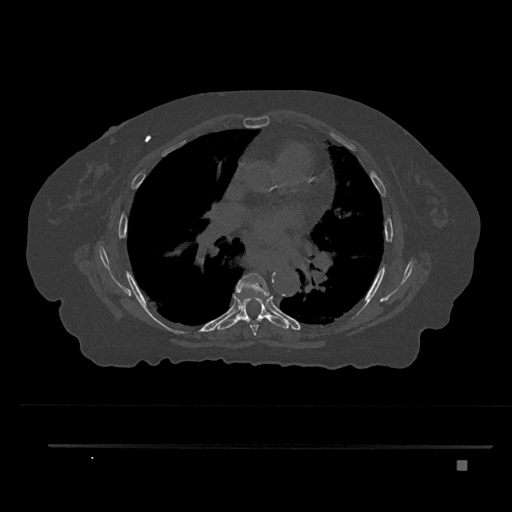
CT including the spine, one axial slice; slice 504 of 797 in the series (ordered by position); reconstruction kernel Br40s/3; 120 kVp; bone window (W 1800 / L 400 HU); 512 × 512 image matrix, field of view 437 × 437 mm. Patient: female, 76 years. Case-level facts recorded for this patient, not image findings: primary cancer: lung; vertebrae with lytic lesions (as recorded): T11, L3.
Structures marked on this image (semi-automatically segmented with operator editing):
- T6 vertebra: bounding box [x1, y1, x2, y2] px = [236, 273, 270, 336]
- T7 vertebra: [218, 298, 289, 330]